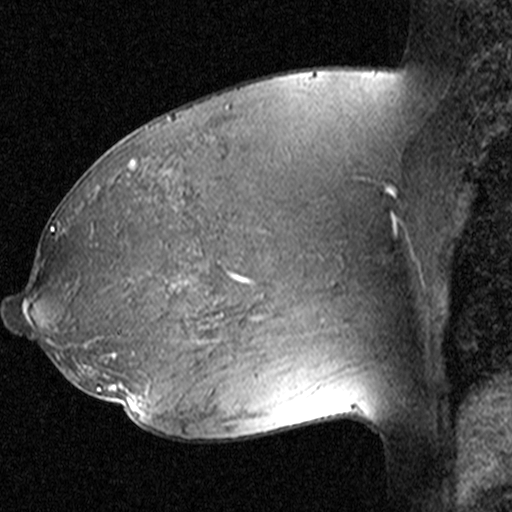
Breast MRI (dynamic contrast-enhanced), one sagittal slice; position 24 of 44 along the scan axis; dynamic contrast-enhanced study with each time point stored as its own series, time point 2 of 3 at this slice position (early post-contrast, ordered by acquisition time); 1.5 T; TE 4.5 ms, TR 11 ms; 512 × 512 image matrix. Patient: female, 38 years. Case-level facts recorded for this patient, not image findings: setting: breast cancer imaged before/during neoadjuvant chemotherapy; receptor status: HR-positive, HER2-negative.
Structures marked on this image (semi-automatically segmented with operator editing):
- analysis volume of interest (the breast-tissue region the enhancement analysis was run in; not a lesion): bounding box [x1, y1, x2, y2] px = [152, 236, 253, 335]
- tumour enhancement mask (voxels above the 90 % enhancement threshold inside the analysis volume of interest): [231, 275, 234, 277]